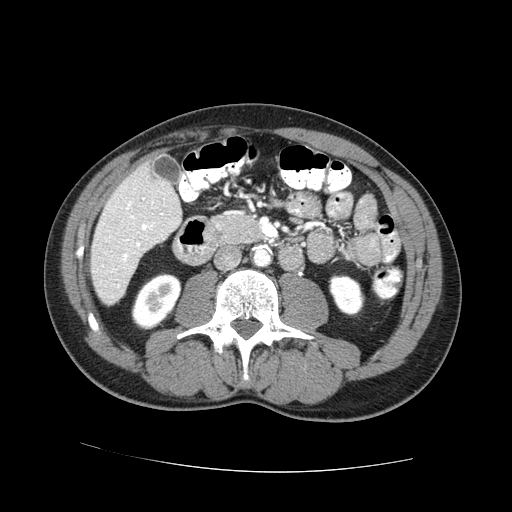
Contrast-enhanced abdominal CT (liver protocol), one axial slice. Slice 18 of 73 in the series (ordered by position). One of 2 acquisitions stored at this slice position. Soft-tissue window (W 400 / L 40 HU). 2.5 mm slice thickness. 512 × 512 image matrix. Case-level facts recorded for this patient, not image findings: diagnosis: hepatocellular carcinoma (patient treated with transarterial chemoembolisation; whether this scan precedes or follows treatment is not stated here); TNM stage (as recorded): Stage-IVA; Child-Pugh class: A; tumour nodularity: uninodular.
Annotated regions visible in this slice (semi-automatically segmented with operator editing):
- liver parenchyma outside the tumour (the mass and vessels are separate outlines, so this box may not span the whole liver): bounding box (x1, y1, x2, y2) in pixels: (90, 160, 182, 304)
- liver vessels: (123, 198, 151, 261)